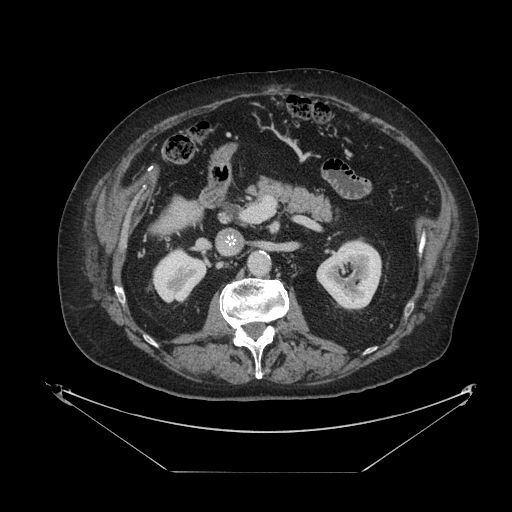
Contrast-enhanced abdominal CT, one axial slice. Position 38 of 121 along the scan axis. Reconstruction kernel STANDARD. 120 kVp. Intravenous contrast given. Soft-tissue window (W 400 / L 40 HU). 2.5 mm slice thickness. 512 × 512 image matrix. Male patient, age 68 years. From the clinical record (not read from this slice): diagnosis: colorectal cancer liver metastases, imaged before liver resection; multiple liver metastases: no; largest metastasis: 4 cm; chemotherapy before resection: yes.
Outlined on this slice (manually delineated by an expert):
- liver: bounding box [x1, y1, x2, y2] px = [158, 200, 198, 230]
- planned liver remnant (the part of the liver to remain after resection): [158, 200, 198, 230]